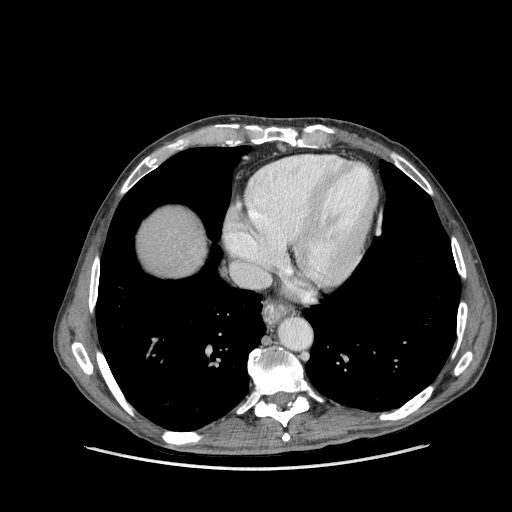
Contrast-enhanced abdominal CT (liver protocol), one axial slice; position 143 of 162 along the scan axis; reconstruction kernel STANDARD; soft-tissue window (W 400 / L 40 HU); 2.5 mm slice thickness; 512 × 512 image matrix, field of view 400 × 400 mm. Case-level facts recorded for this patient, not image findings: diagnosis: hepatocellular carcinoma (patient treated with transarterial chemoembolisation; whether this scan precedes or follows treatment is not stated here); TNM stage (as recorded): Stage-IIIA; Child-Pugh class: A.
Structures marked on this image (semi-automatic segmentation, software-assisted and operator-edited):
- liver parenchyma outside the tumour (the mass and vessels are separate outlines, so this box may not span the whole liver): box from (x=138, y=208) to (x=206, y=276) px